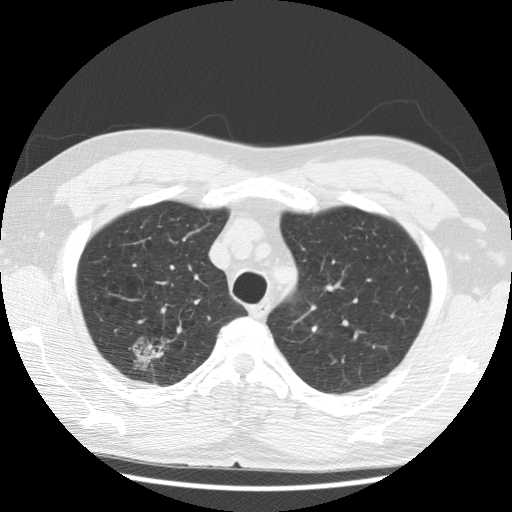
Low-dose screening chest CT, axial slice. Baseline screening round. Lung window (W 1500 / L -600 HU). 2.5 mm slice thickness. Slice 28 of 122 in the series. 512 × 512 image matrix, field of view 350 × 350 mm. Male, age 59 years at enrolment.
• Expert-annotated lung lesion, bounding box <110,324,178,388> (left, top, right, bottom; pixels).
• Reader record for this screening exam (exam-level; its link to the box is not recorded): non-calcified nodule or mass ≥4 mm, right upper lobe, 30 × 28 mm, poorly defined margins, ground glass attenuation.